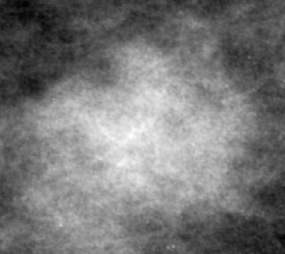
Cropped region of a digitized screen-film mammogram centred on a radiologist-marked abnormality, right breast, CC view, BI-RADS breast density category 1 (scale 1–4).
Marked abnormality: mass, shape irregular, margins ill defined; BI-RADS assessment category 5; subtlety rating 5 on a 1 (subtle) to 5 (obvious) scale; pathology result (as recorded, not read from the image): malignant.